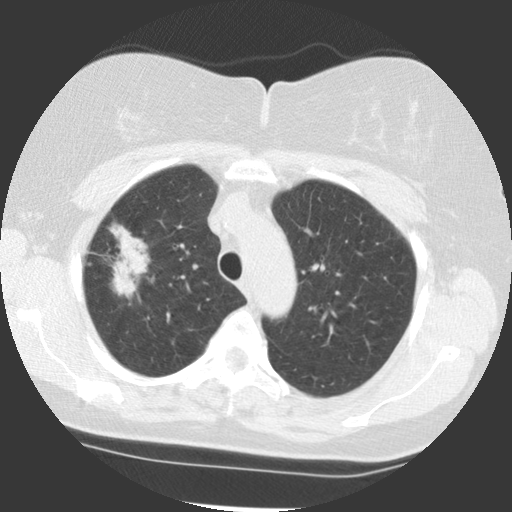
Low-dose screening chest CT, one axial slice; slice 89 of 113 in the series (ordered by position); reconstruction kernel STANDARD; lung window (W 1500 / L -600 HU); 512 × 512 image matrix, field of view 320 × 320 mm.
Outlined on this slice (outlined manually by an expert reader):
- lesion 1 (tumor, upper lobe of right lung): bounding box <109,223,150,299> (left, top, right, bottom; pixels)